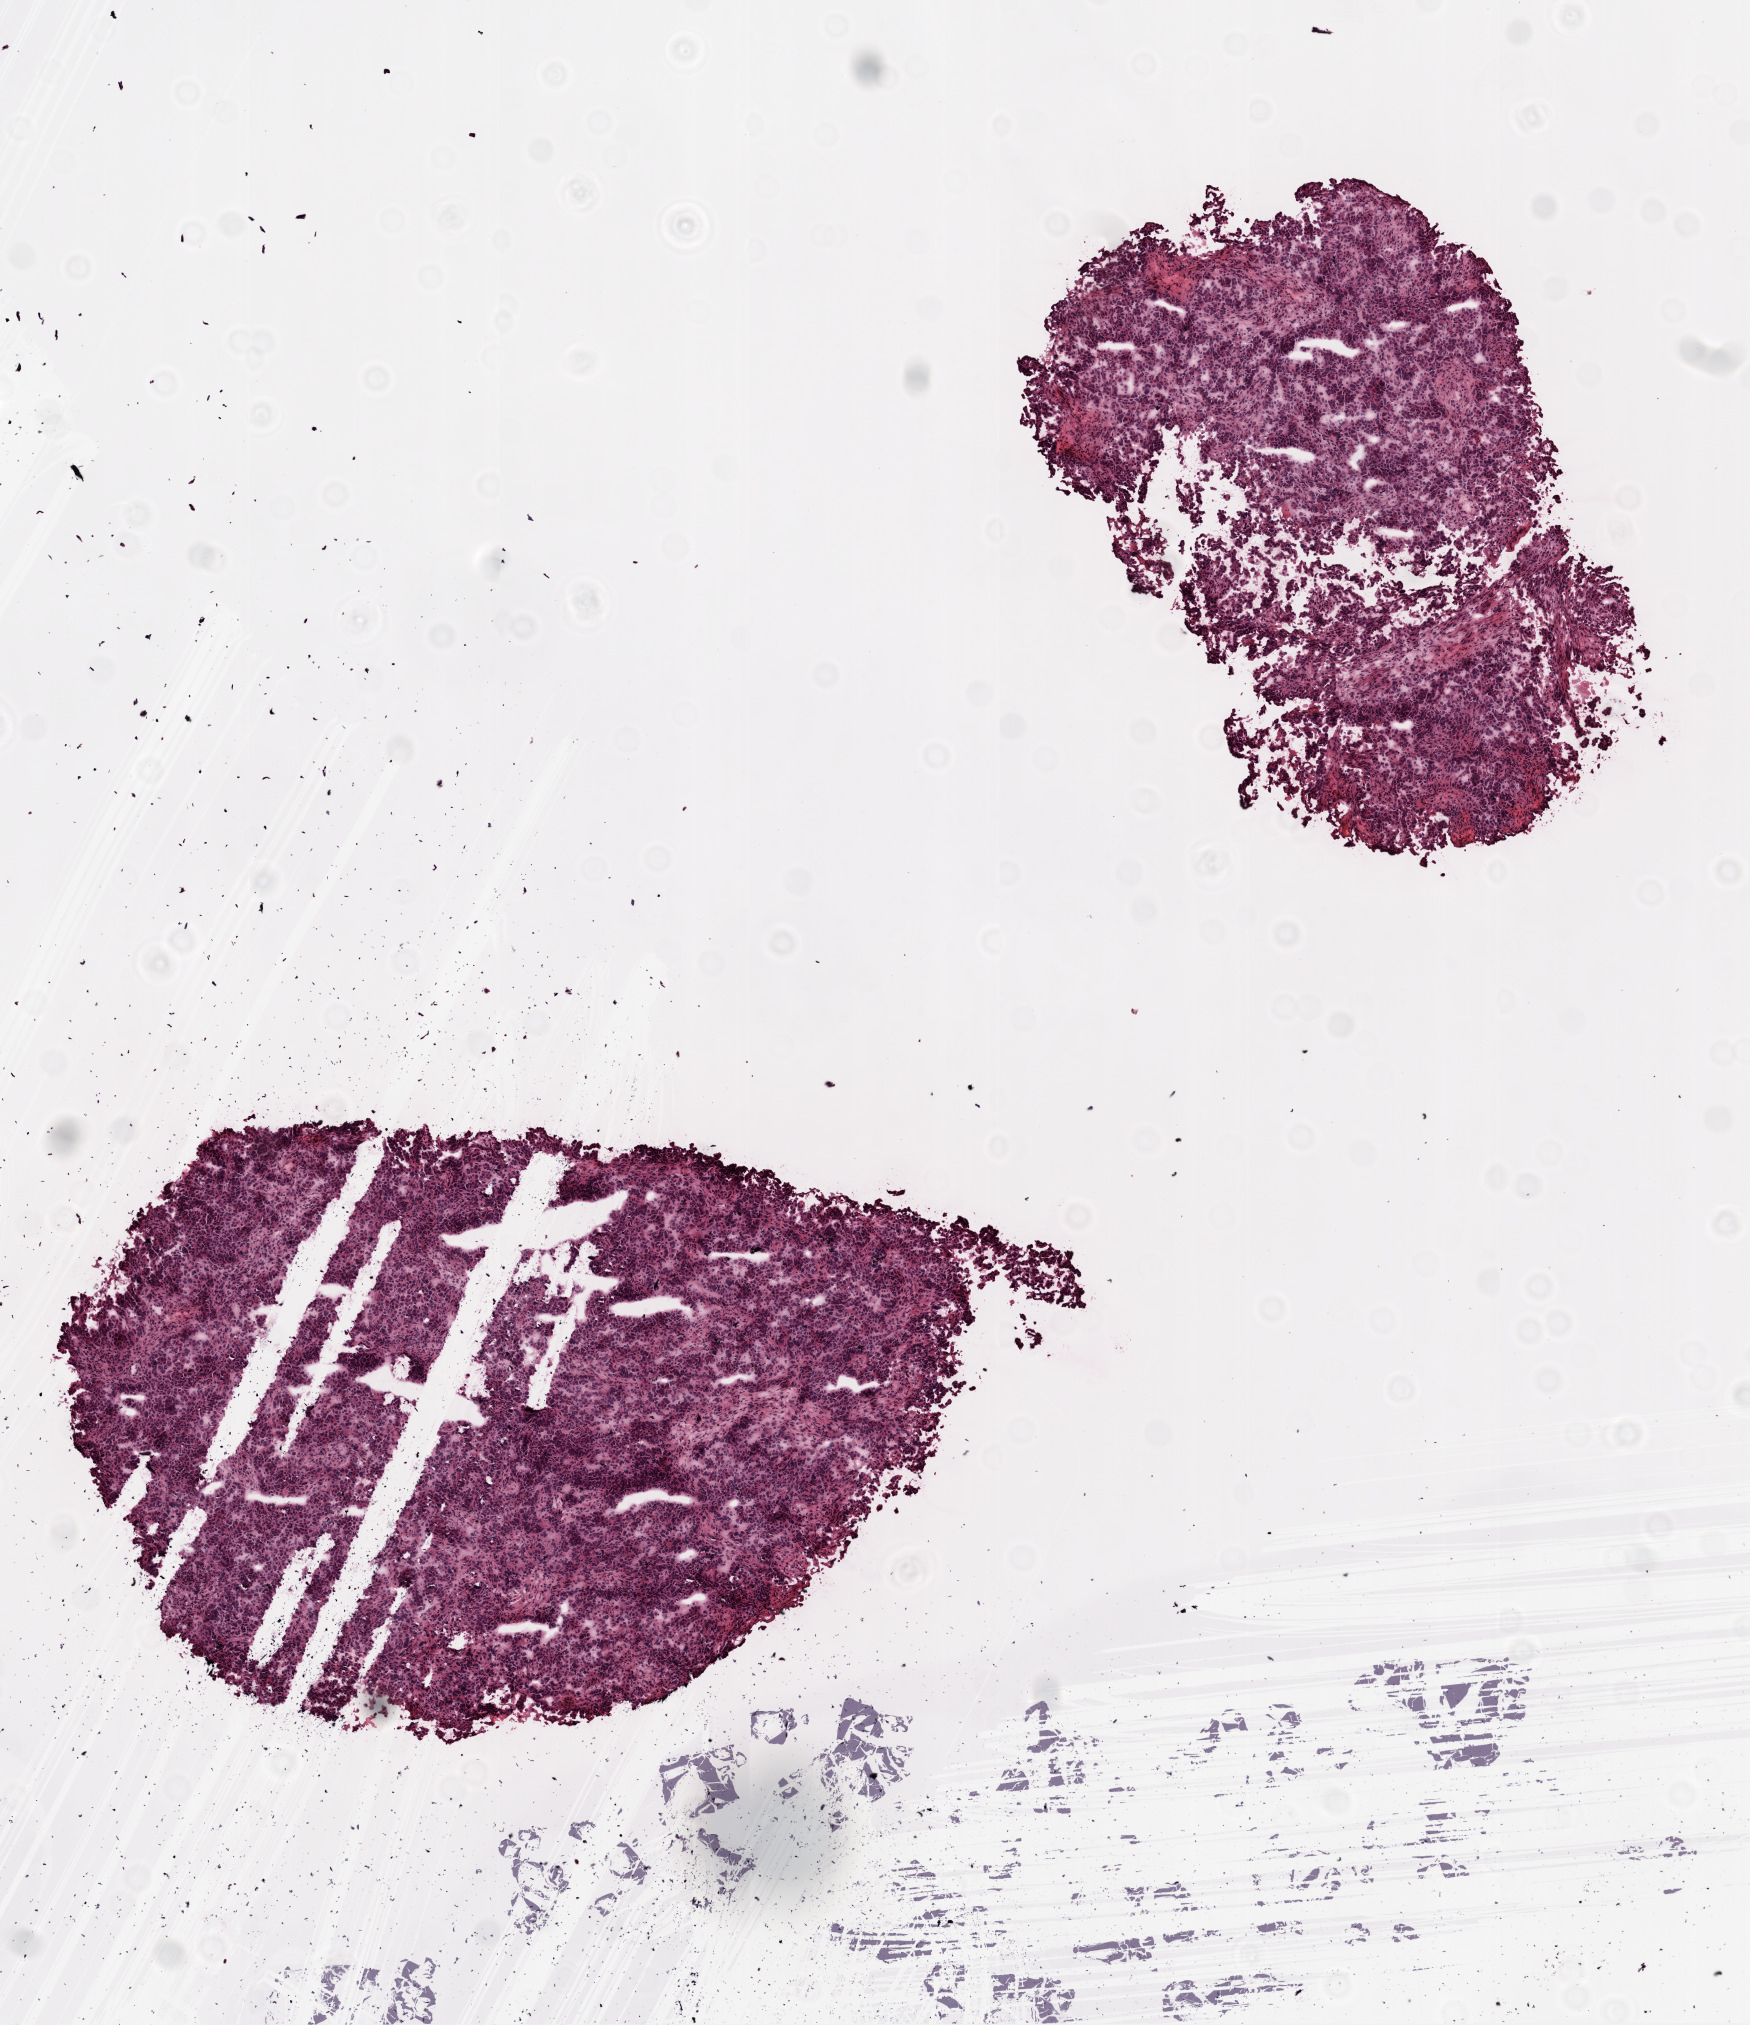
Digitized Hematoxylin and eosin (H&E) stained tissue section (whole slide) — whole scanned area (about 7.0 x 8.1 mm, slide scanned at 20x) shown as a low-resolution overview. Frozen section from the top of the tissue portion. Ovary, recurrent tumour sample. Female, age 54 years at initial diagnosis.
This section: recurrent tumour. Patient diagnosis: Serous cystadenocarcinoma, NOS.